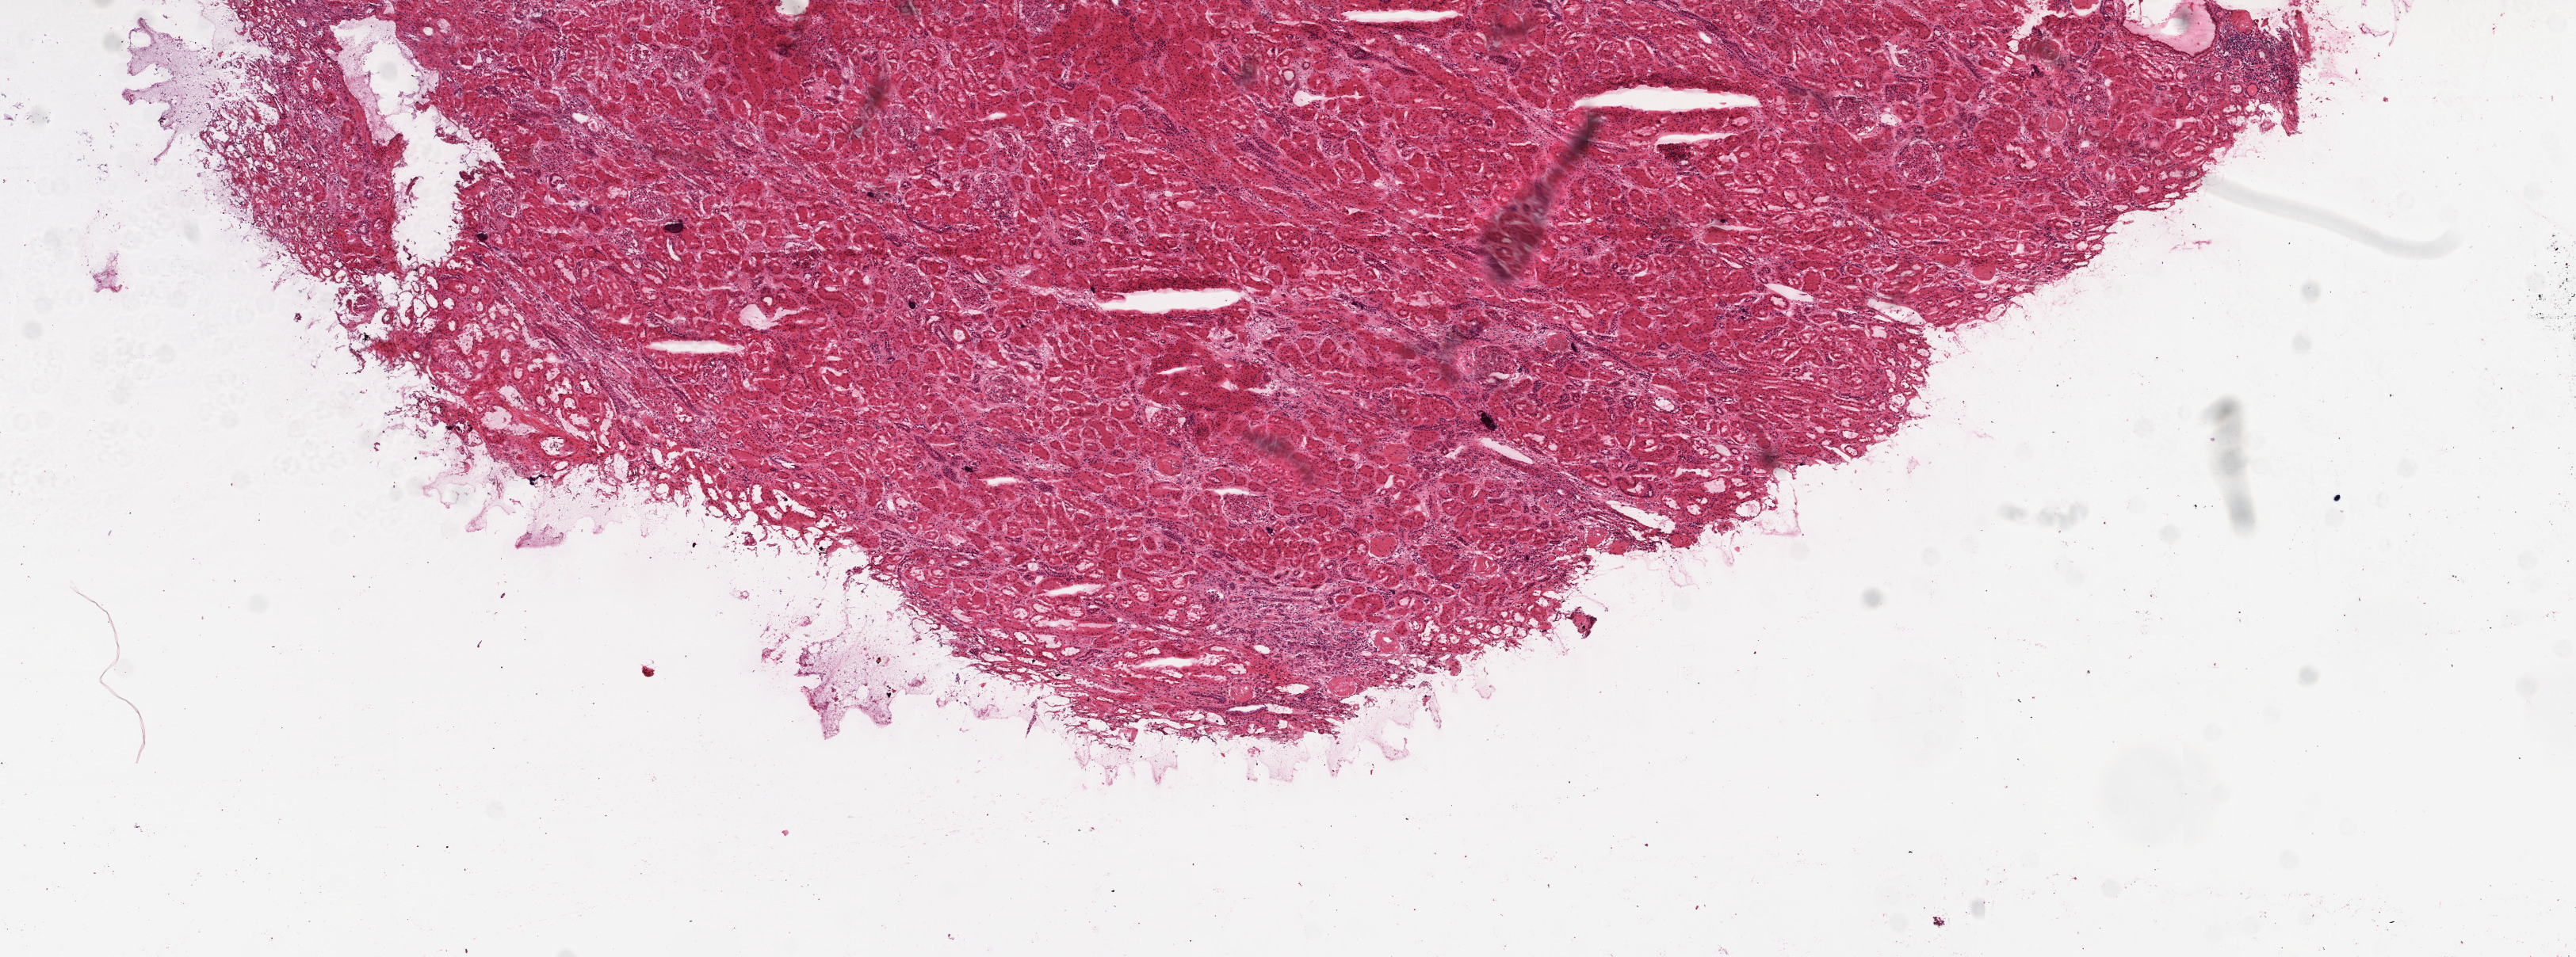
Digitized H&E-stained tissue section (whole slide), low-resolution overview of the scanned area, about 13.0 x 4.8 mm (from a 20x scan), frozen section, kidney, solid tissue normal (non-tumour tissue) sample. Patient: female, age at initial diagnosis 71 years.
This section: solid tissue normal (non-tumour) sample from the same patient. Patient diagnosis: Clear cell adenocarcinoma, NOS.